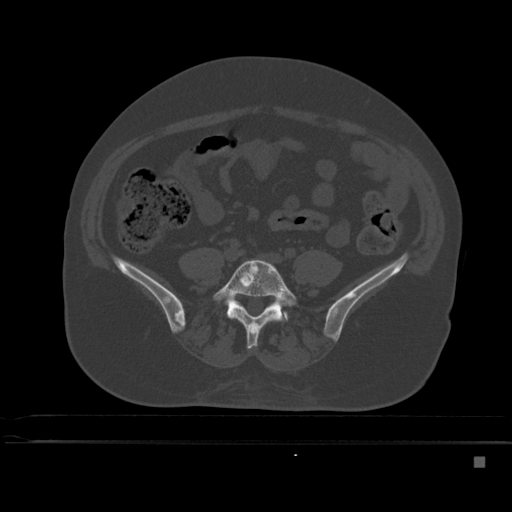
CT including the spine, one axial slice; bone window (W 1800 / L 400 HU); 1.5 mm slice thickness; 512 × 512 image matrix. Female patient, age 33 years. Case-level facts recorded for this patient, not image findings: primary cancer: breast; vertebrae with lytic lesions (as recorded): T1.
Annotated regions visible in this slice (semi-automatic segmentation, software-assisted and operator-edited):
- L5 vertebra: bounding box (x1, y1, x2, y2) in pixels: (212, 259, 298, 349)